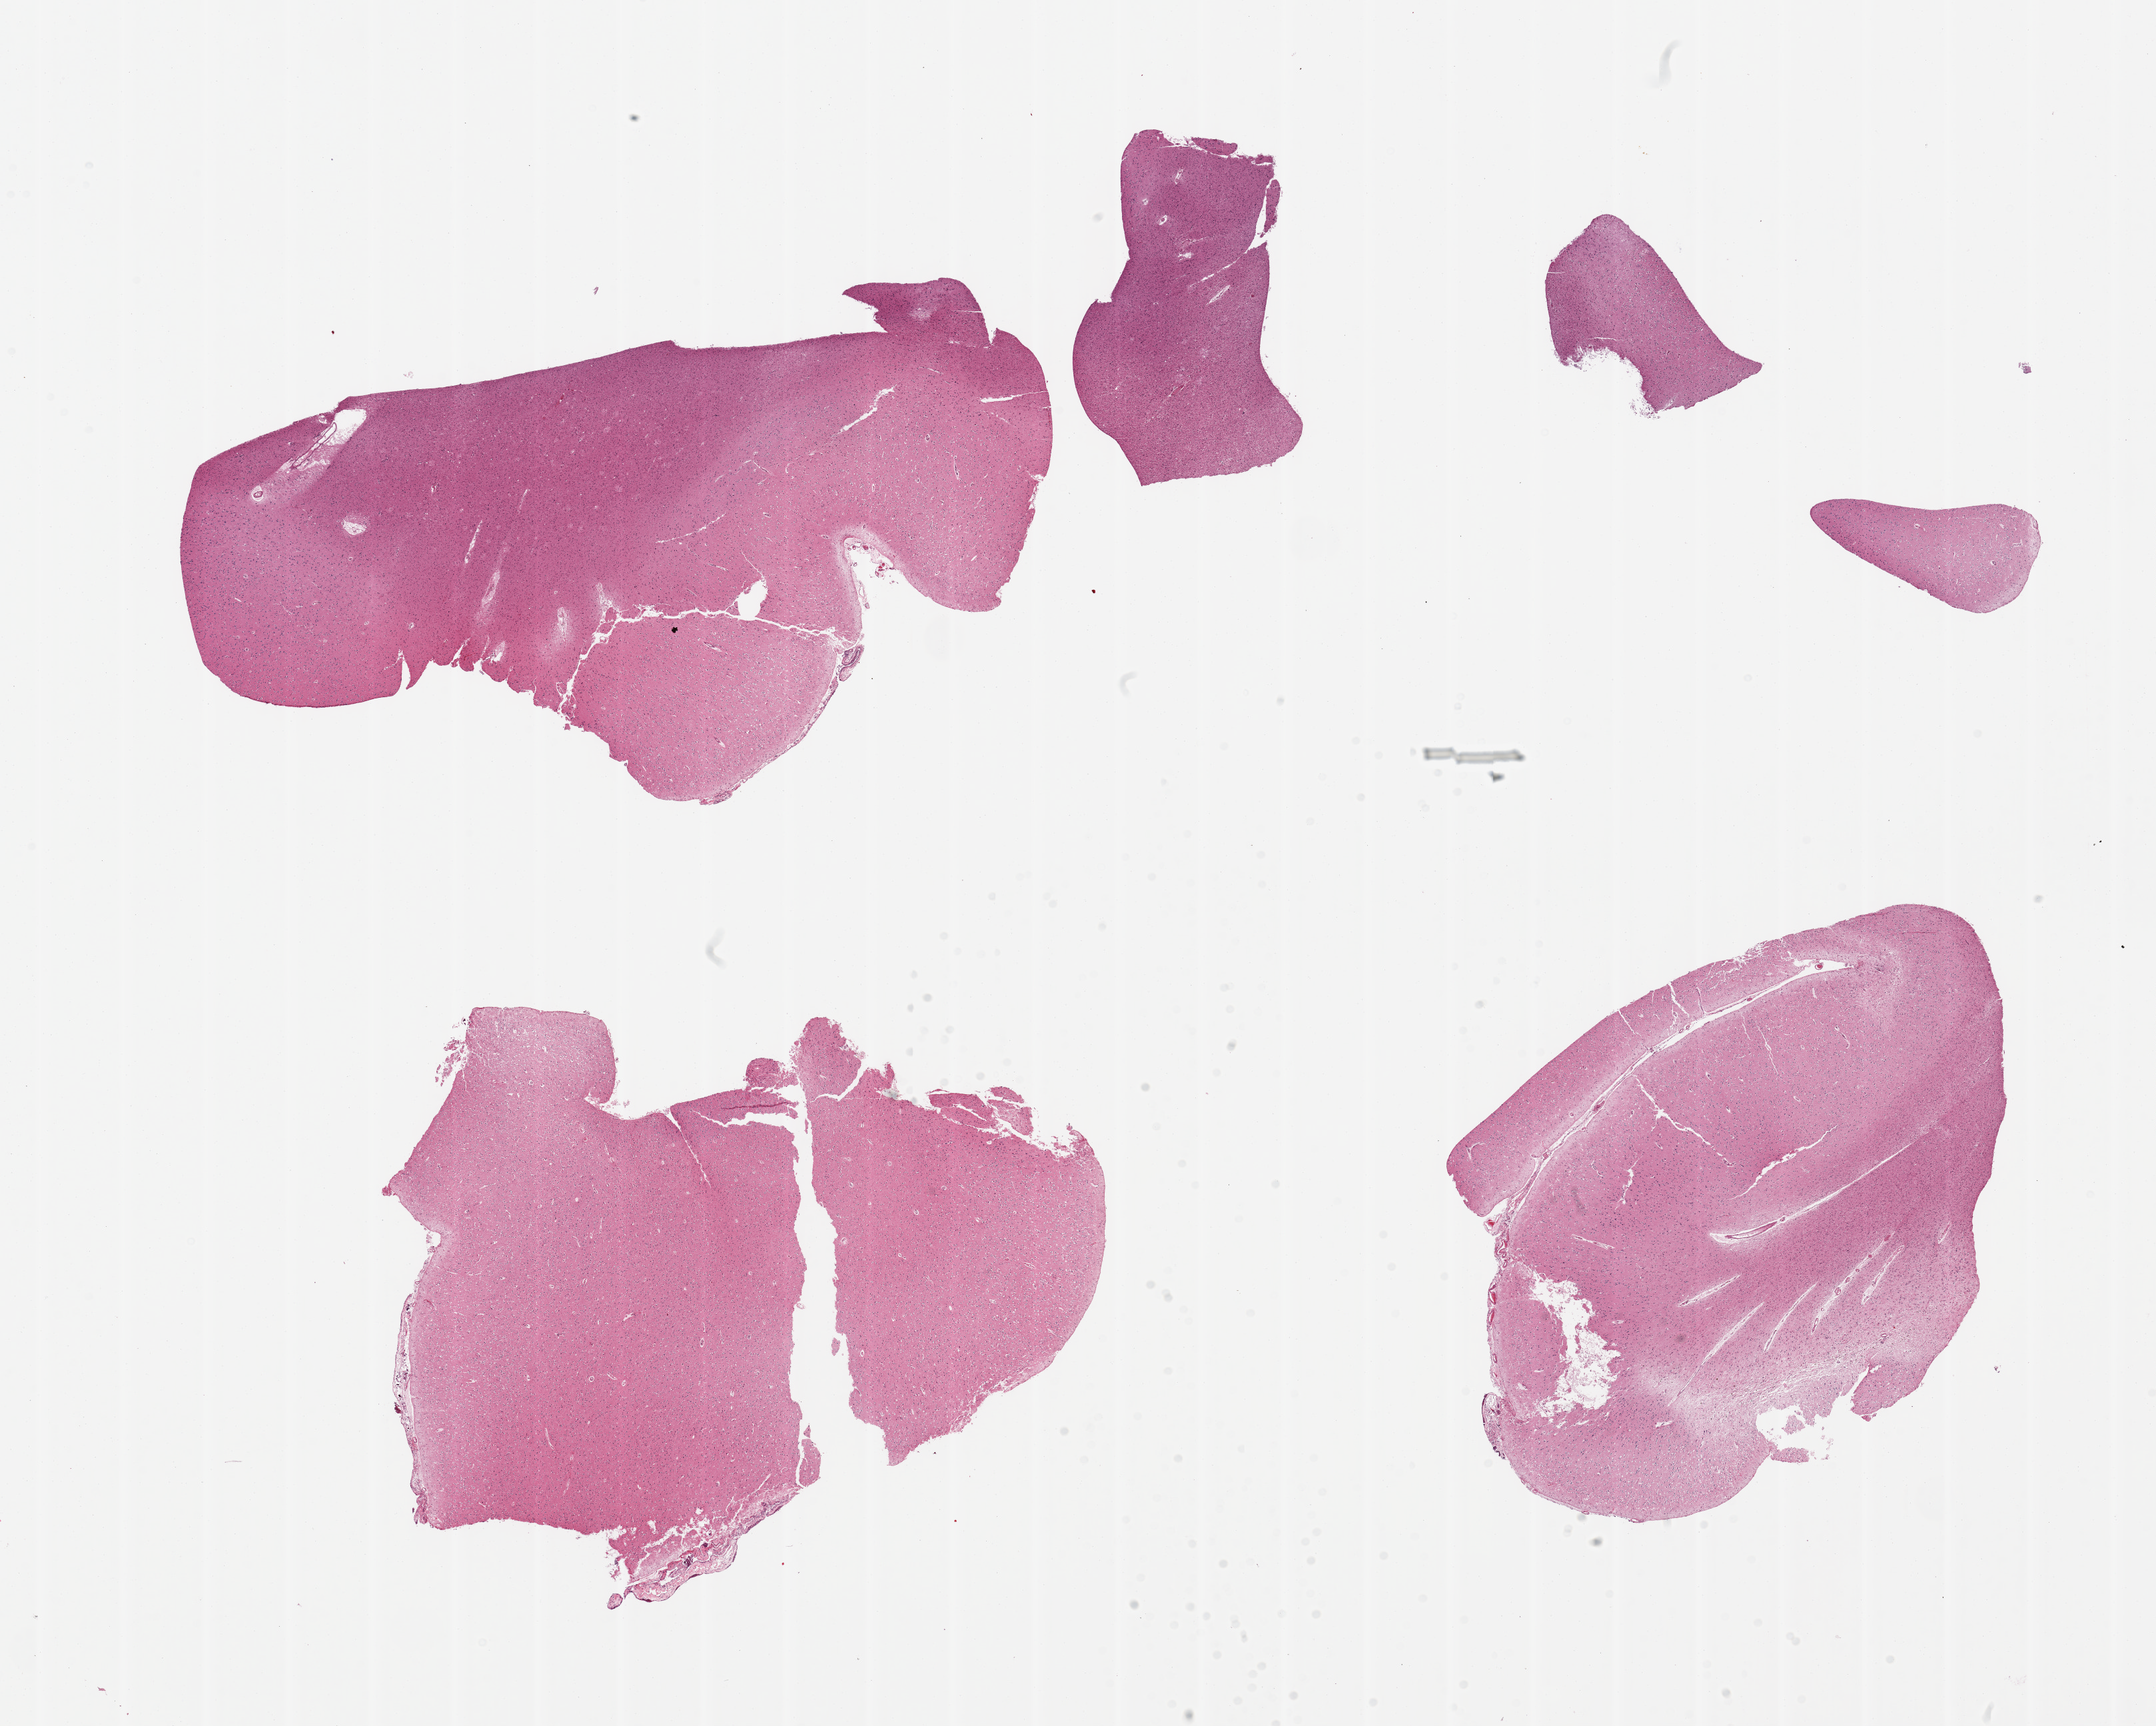
H&E whole-slide image, low-resolution overview of the scanned area, about 25.6 x 20.5 mm. PAXgene-fixed paraffin-embedded (PFPE) section. Section of cerebral cortex (target tissue). Donor tissue sample. Donor: male.
• pathologist's review note for this sample: 4 pieces (fragmented) no abnormalities